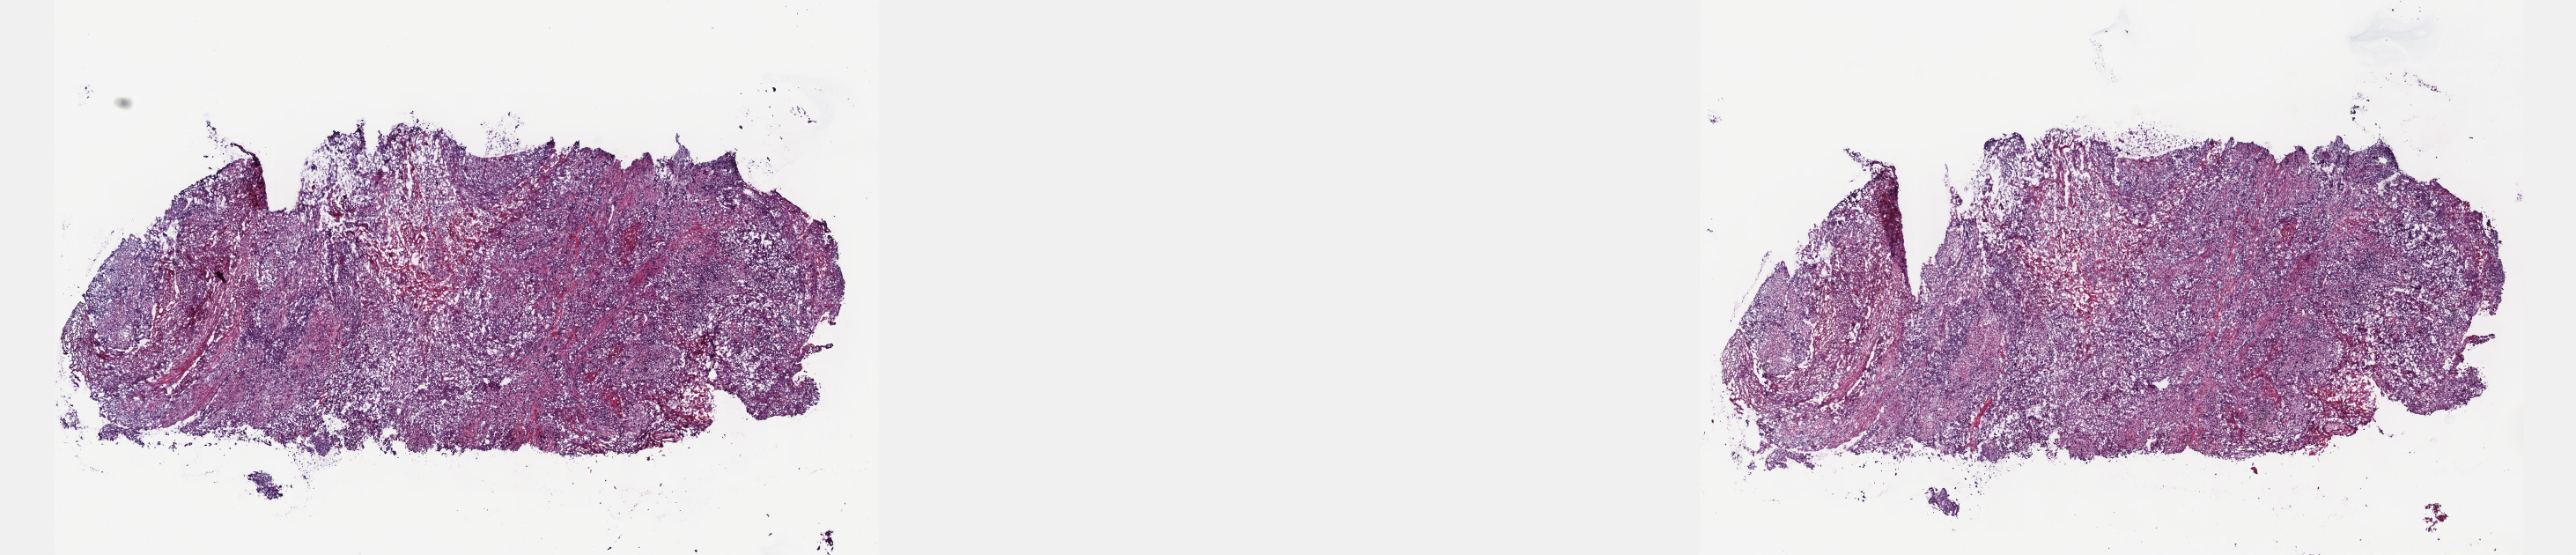
H&E-stained whole-slide image — shown as a low-resolution overview of the whole scanned area (about 23.6 x 5.1 mm, slide scanned at 40x); frozen section from the top of the tissue portion; primary tumour sample from the bladder. Male patient; age at initial diagnosis 60 years. Histologic grade: high grade. Pathologist review of this section (percent, as recorded): tumour cells 35%, tumour nuclei 60%, normal cells 0%, stromal cells 45%, necrosis 20%. Infiltration values recorded for this section: lymphocyte infiltration 30%, monocyte infiltration 2%, neutrophil infiltration 3%.
TNM: T2 NX M0. Histologic diagnosis: Transitional cell carcinoma. AJCC pathologic stage: II.